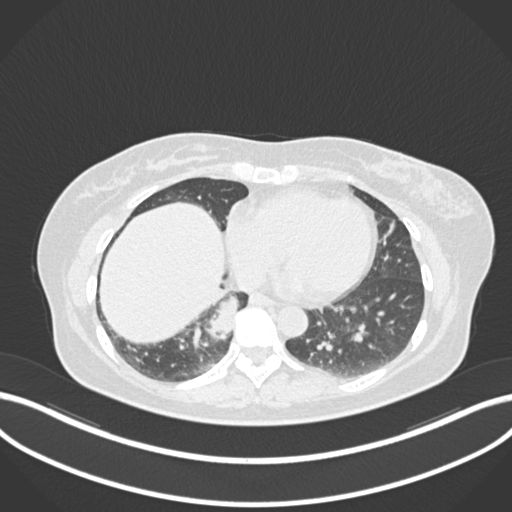
Chest CT, one axial slice; position 547 of 677 along the scan axis; reconstruction kernel B30f; lung window (W 1500 / L -600 HU); 1 mm slice thickness; 512 × 512 image matrix, field of view 400 × 400 mm. Patient: female, 54 years. From the clinical record (not read from this slice): clinical TNM (as recorded): T4 N0 M0.
Annotated regions visible in this slice (bounding box drawn by a radiologist):
- lung tumour (recorded histology: adenocarcinoma): bounding box [x1, y1, x2, y2] px = [207, 295, 246, 342]